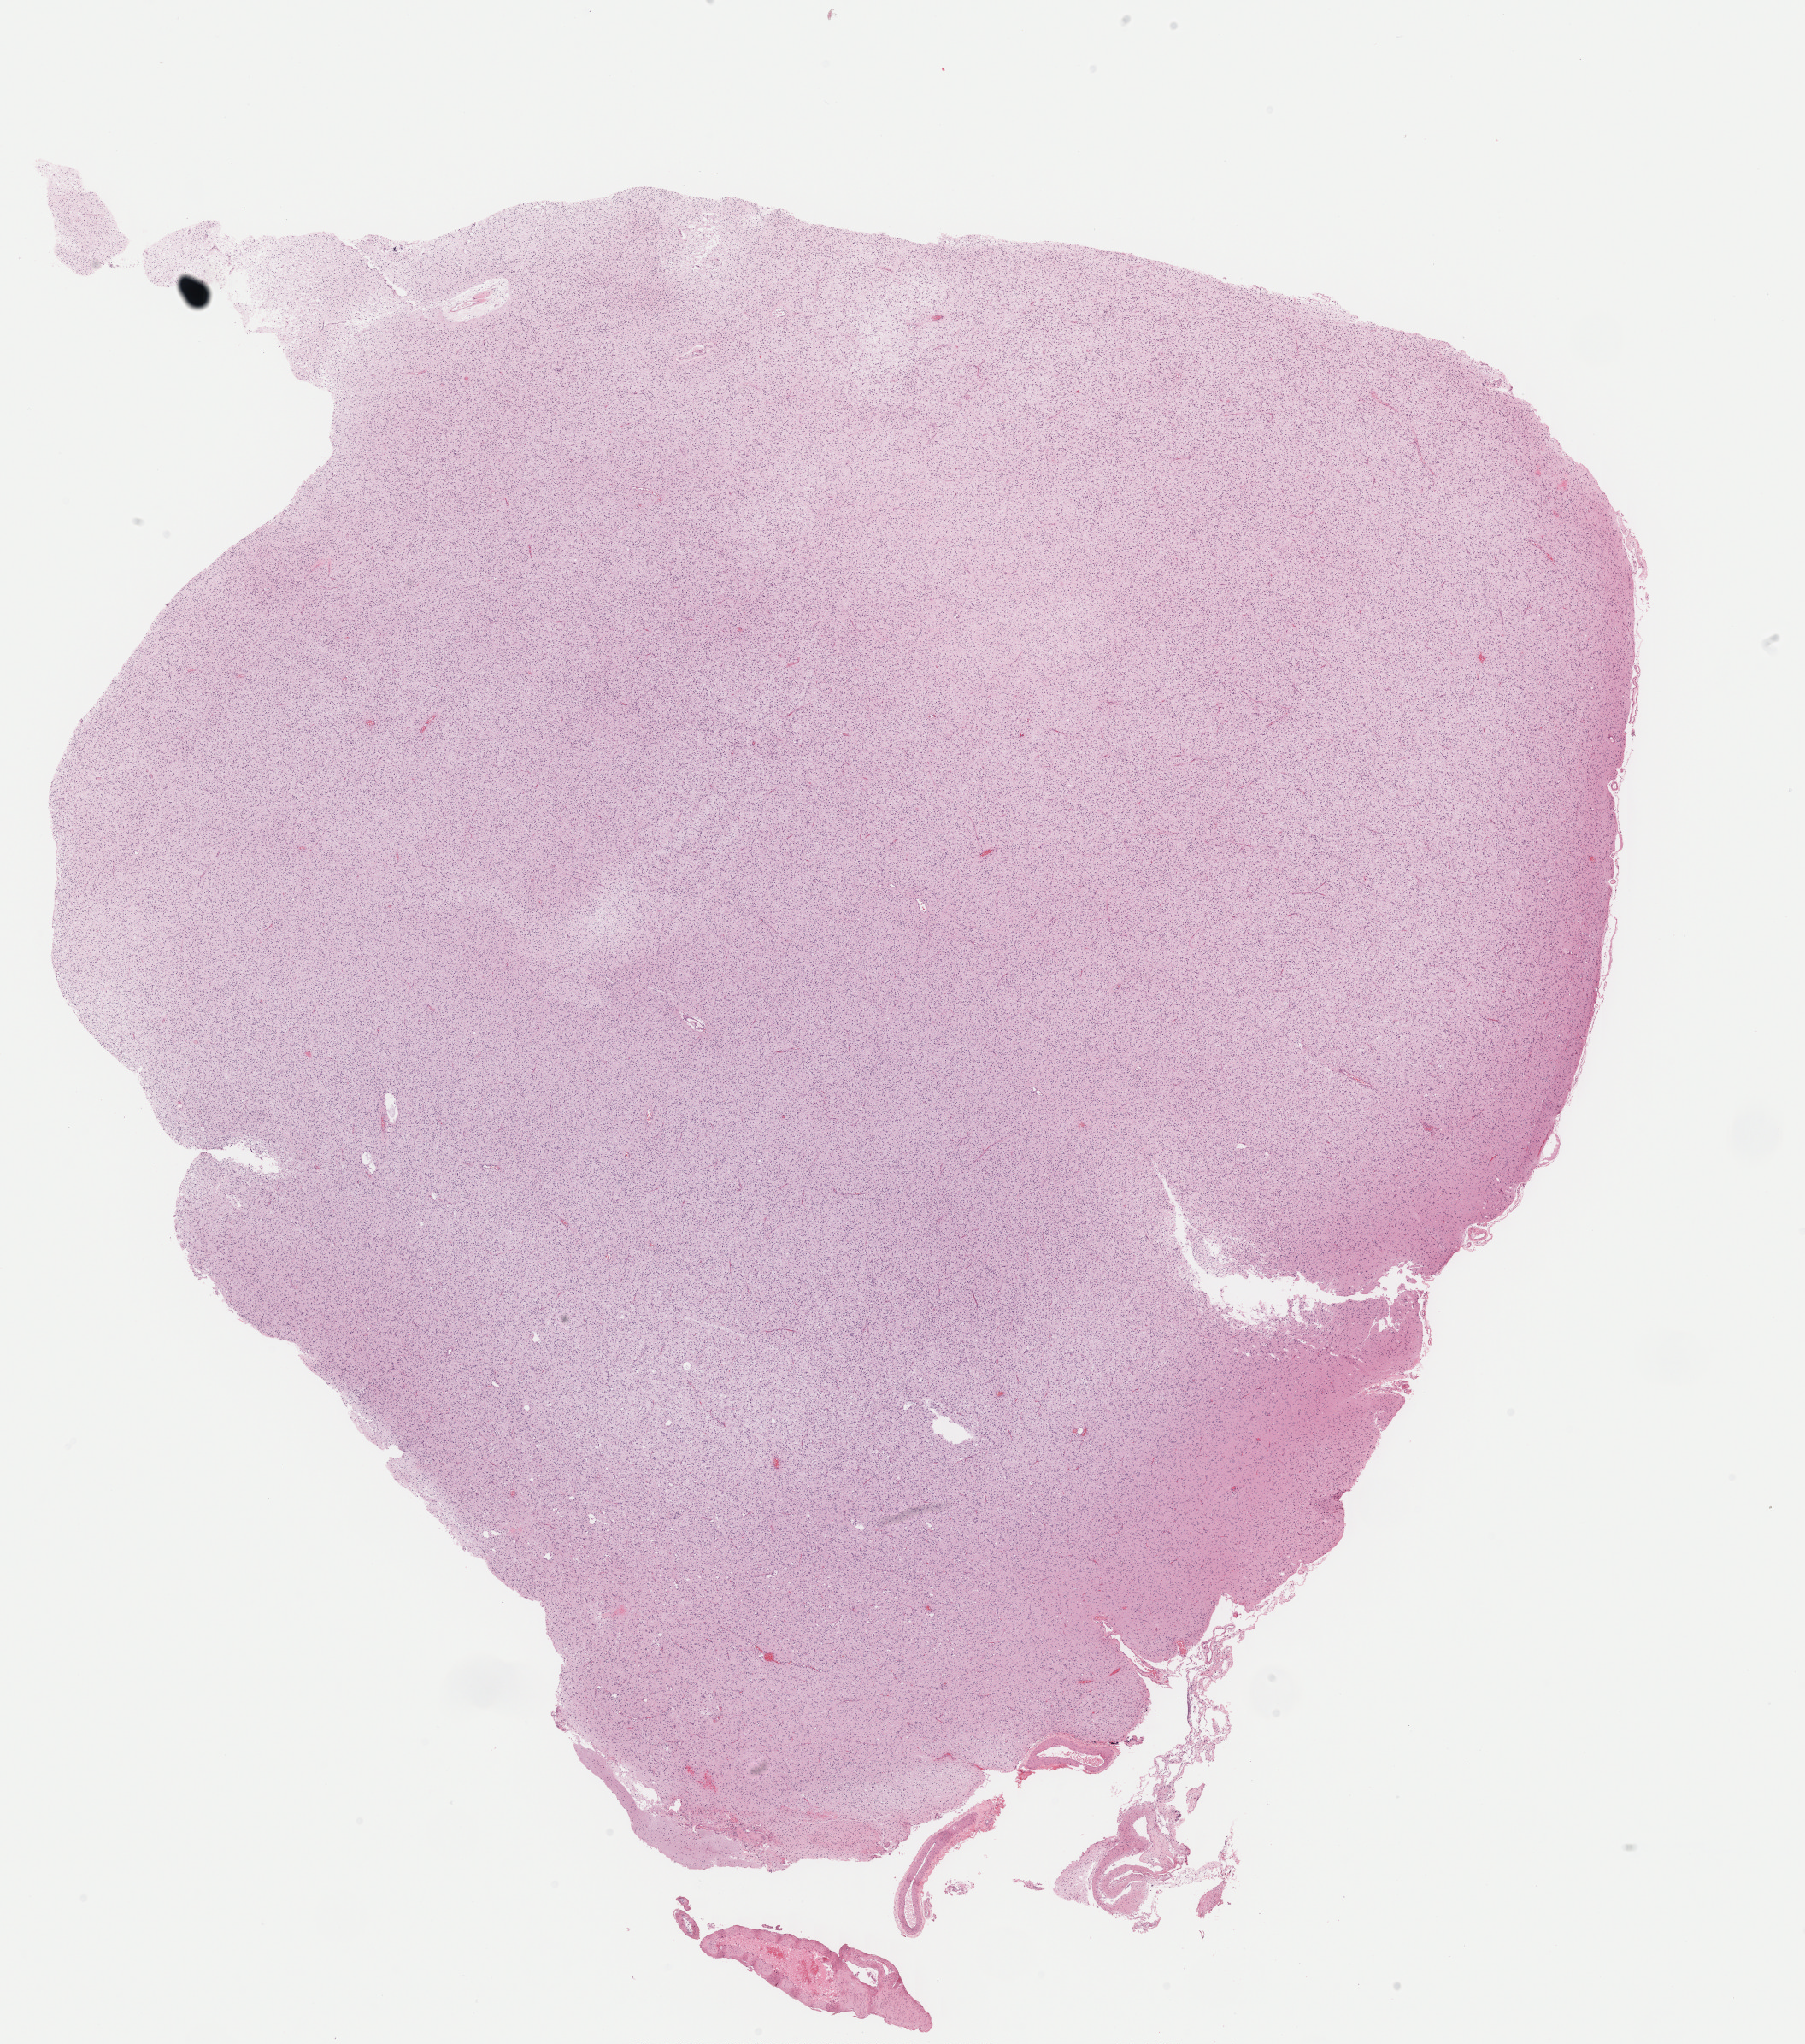
Digitized H&E tissue section (whole slide) — shown as a low-resolution overview of the whole scanned area (about 16.6 x 18.8 mm). Formalin-fixed paraffin-embedded (FFPE) diagnostic section. Primary tumour sample from the brain. Male, age 26 years at initial diagnosis. Histologic grade: G2 (moderately differentiated).
Histologic diagnosis: Mixed glioma.